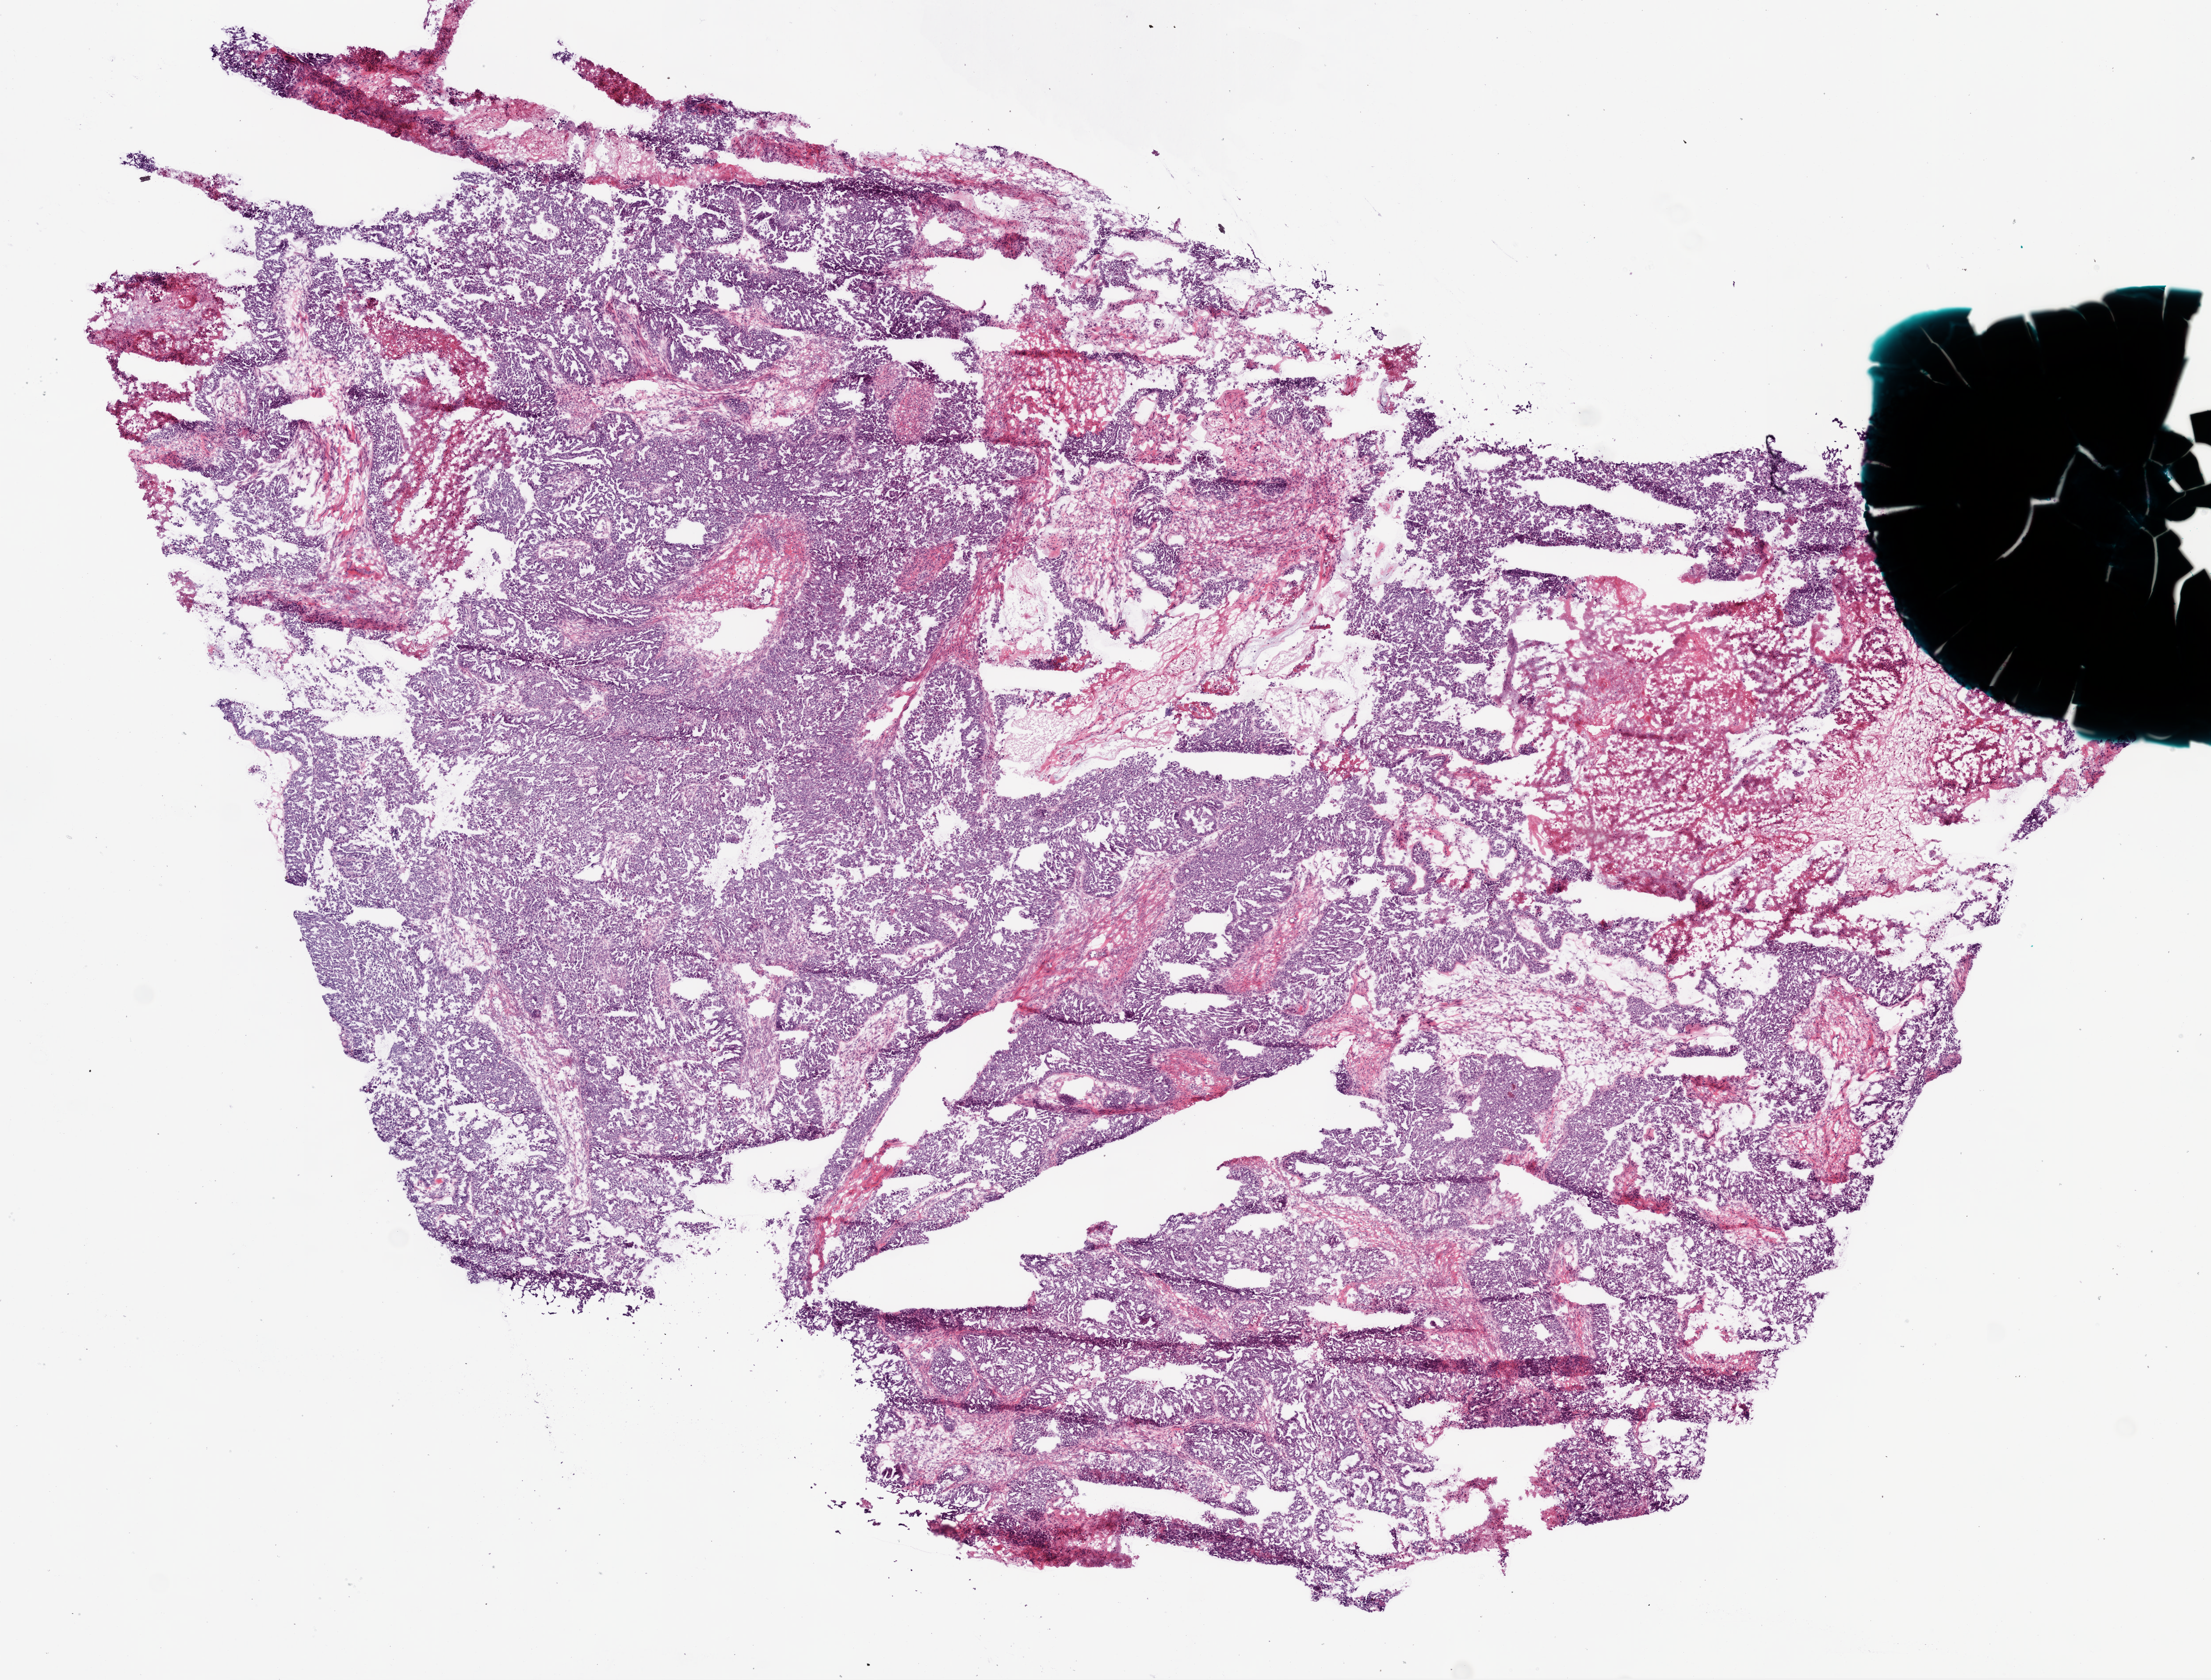
H&E-stained whole-slide image, low-resolution overview of the scanned area, about 10.0 x 7.6 mm, frozen section from the bottom of the tissue portion, sample: primary tumour, ovary. Patient: female, age at initial diagnosis 51 years. Histologic grade: G3 (poorly differentiated). Pathologist review of this section (percent, as recorded): tumour cells 60%, tumour nuclei 85%, normal cells 20%, stromal cells 0%, necrosis 20%.
- histologic diagnosis: Serous cystadenocarcinoma, NOS
- FIGO stage: IIIC